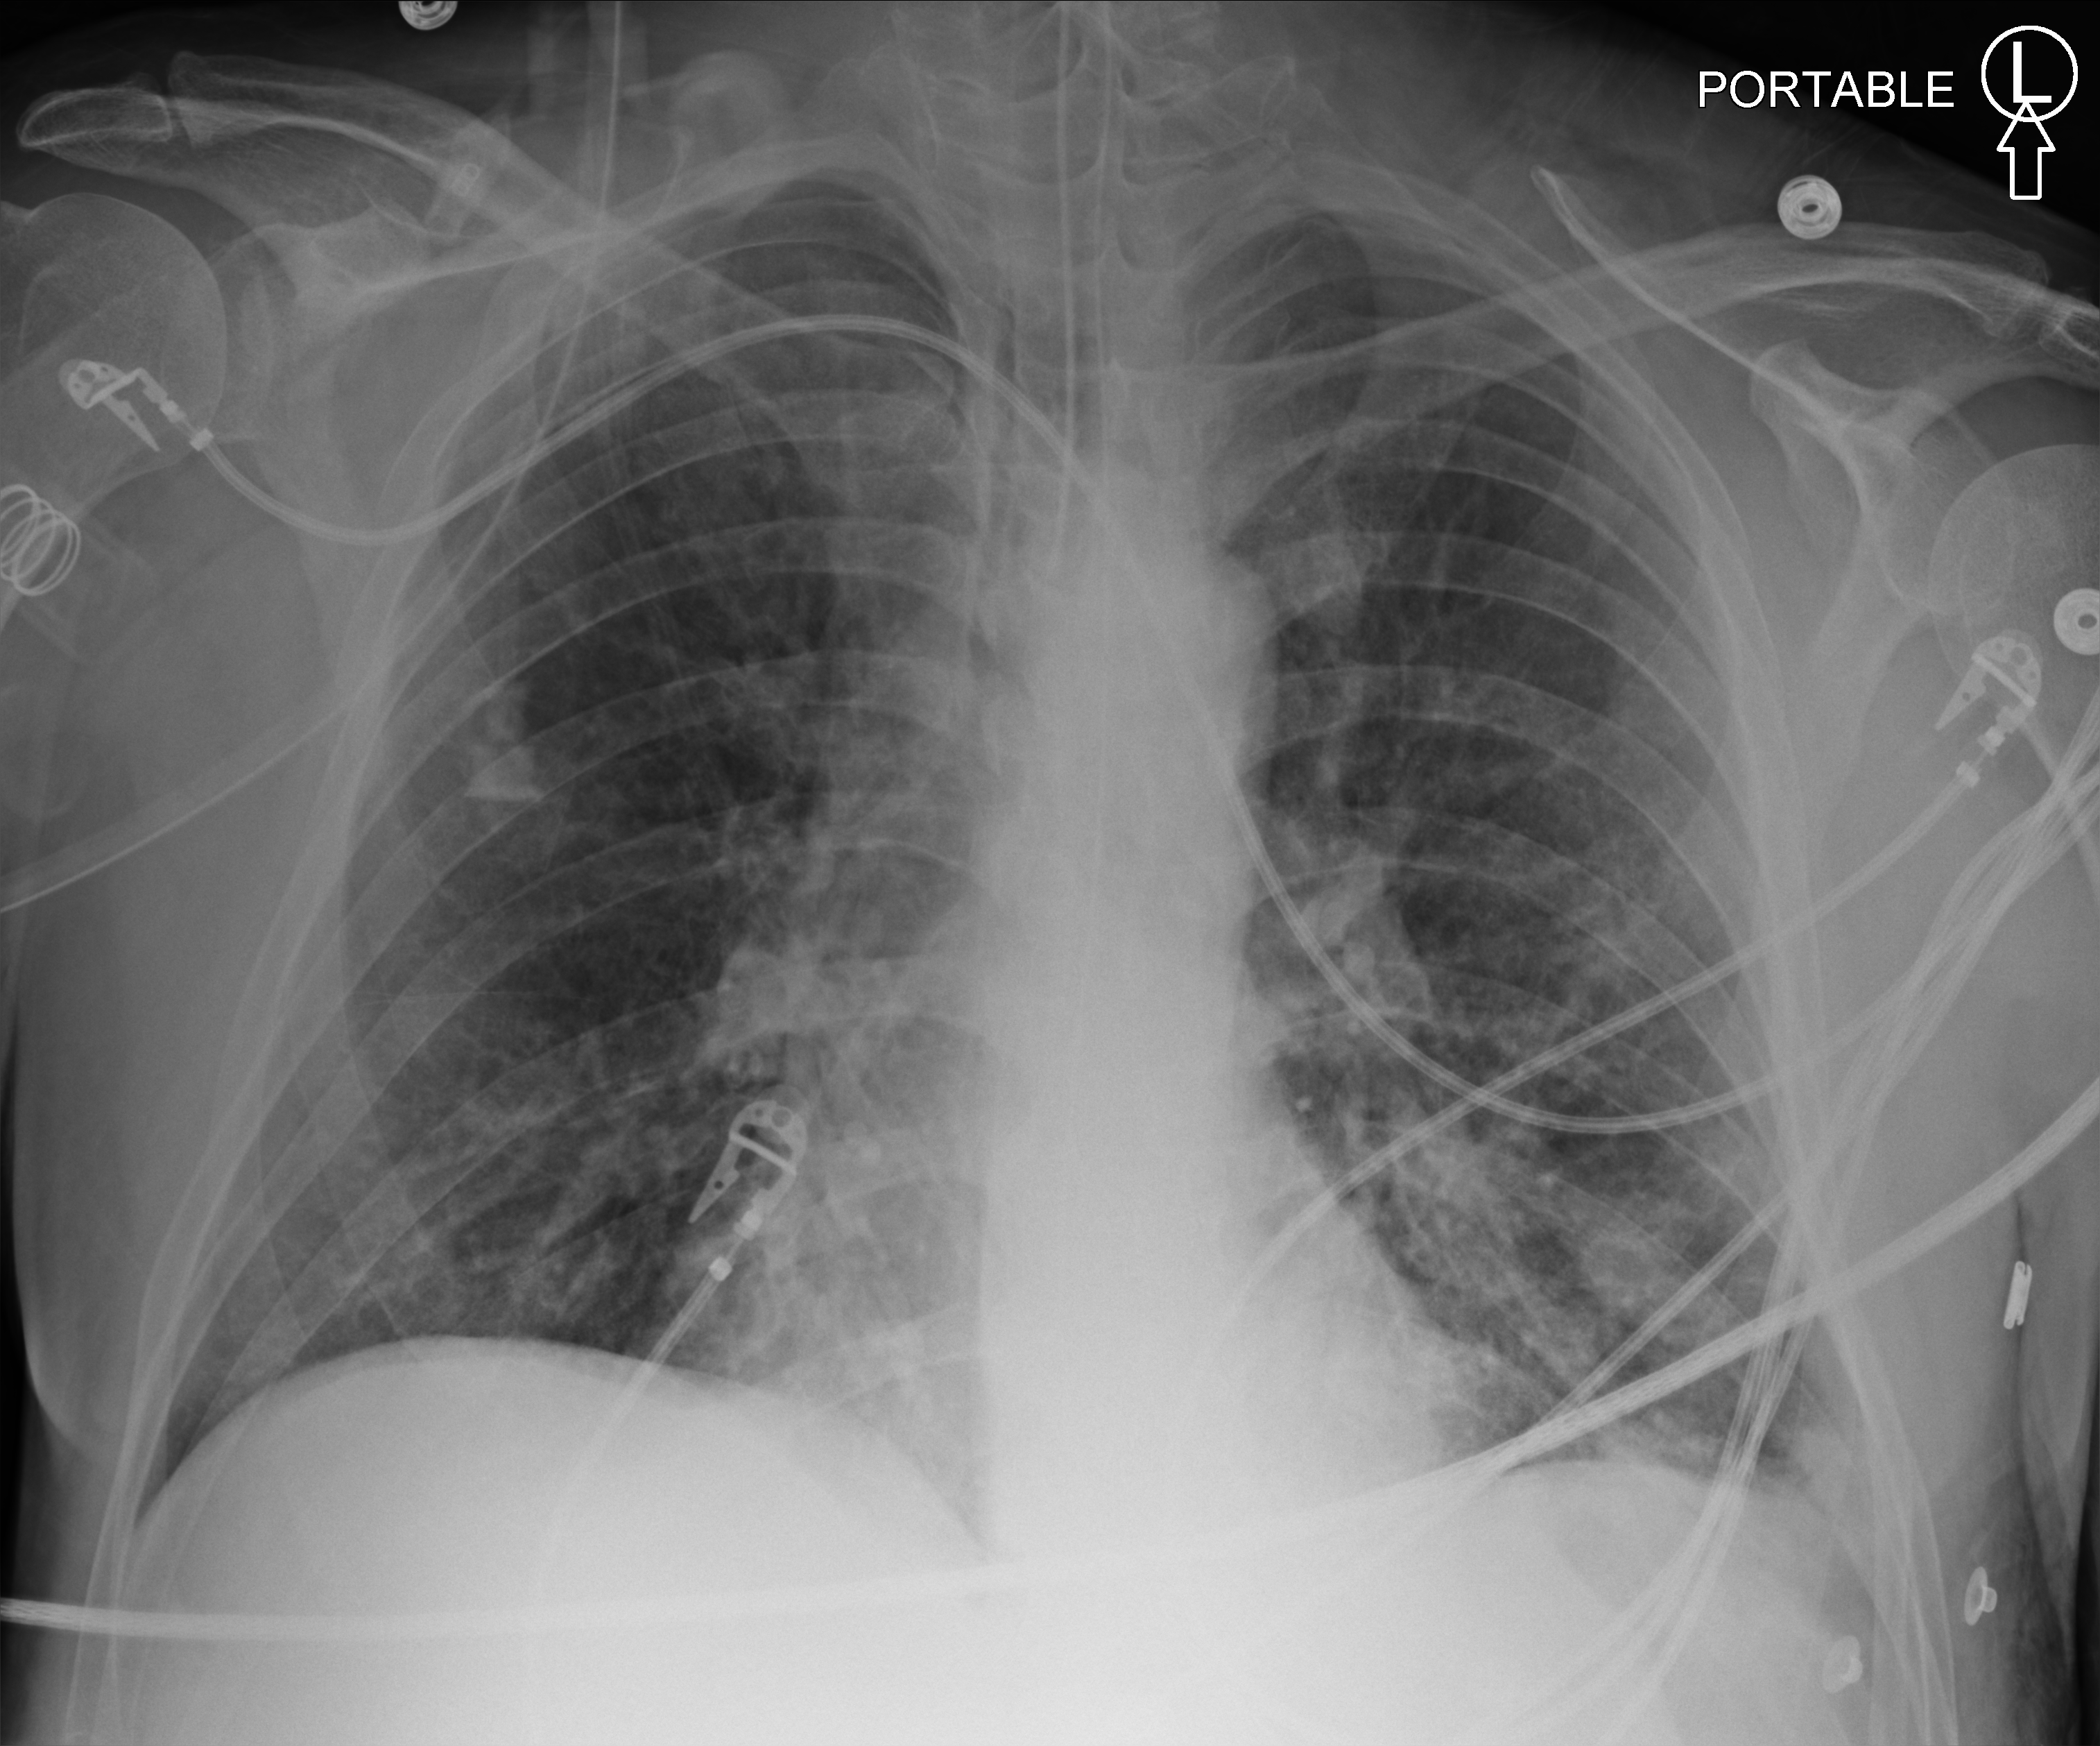
Chest X-ray (portable); anteroposterior (AP) projection. Male patient hospitalised with COVID-19, age 18–59 years.
From the hospital-stay record, not from the radiograph (when in the stay this image was taken is not recorded): other chronic lung disease (admission record): no; admitted to intensive care during this hospital stay: no; mechanically ventilated during this hospital stay: yes.